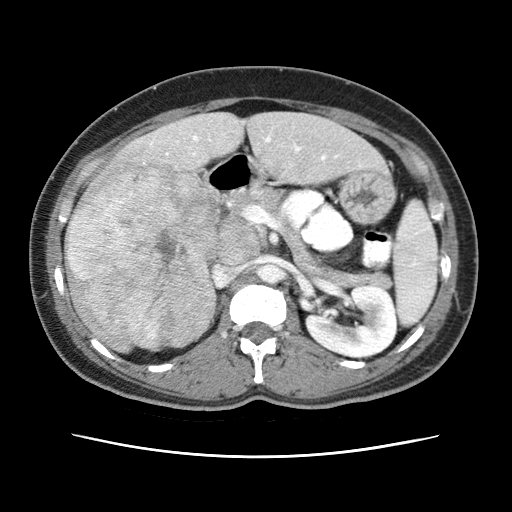
Contrast-enhanced abdominal CT (liver protocol), one axial slice; position 23 of 79 along the scan axis; 120 kVp; soft-tissue window (W 400 / L 40 HU); 512 × 512 image matrix, field of view 340 × 340 mm. Case-level facts recorded for this patient, not image findings: diagnosis: hepatocellular carcinoma (patient treated with transarterial chemoembolisation; whether this scan precedes or follows treatment is not stated here); TNM stage (as recorded): Stage-I; Child-Pugh class: A.
Outlined on this slice (semi-automatically segmented with operator editing):
- abdominal aorta: box from (x=261, y=265) to (x=281, y=283) px
- liver parenchyma outside the tumour (the mass and vessels are separate outlines, so this box may not span the whole liver): (x=64, y=112)–(x=382, y=344)
- mass: (x=64, y=159)–(x=216, y=353)
- liver vessels: (x=150, y=136)–(x=338, y=160)